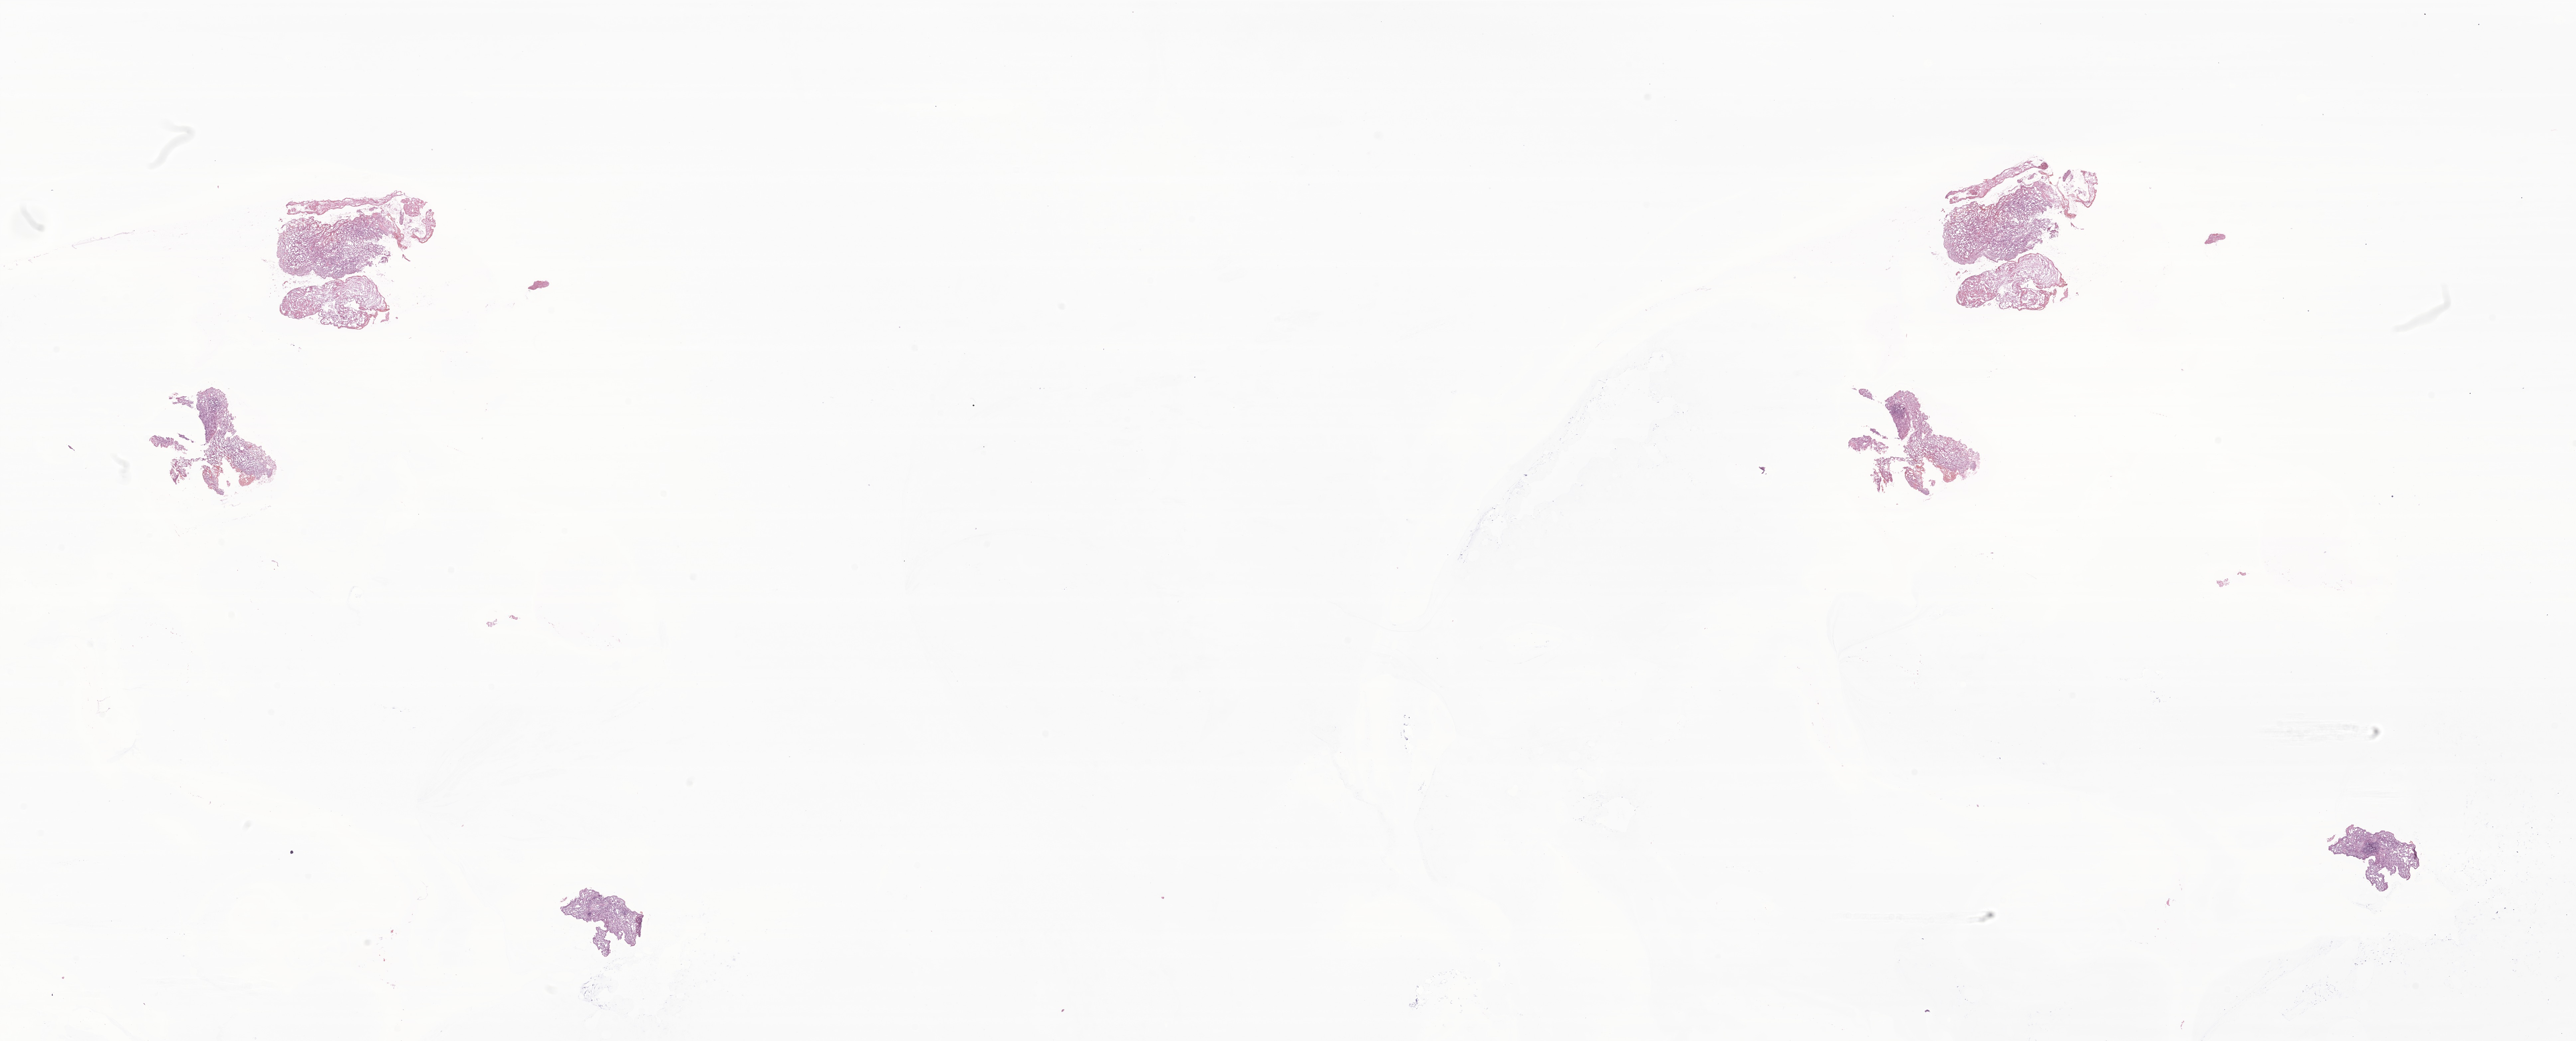
Digitized haematoxylin and eosin-stained section of tumor tissue from the soft tissue of upper extremity — a low-resolution overview of the entire scanned area, about 32.7 x 13.2 mm. Frozen section (OCT-embedded). Patient: female, age 184 months (15 years 4 months).
Recorded diagnosis: Synovial sarcoma, spindle cell. Tissue or organ of origin (case record): connective, subcutaneous and other soft tissues of upper limb and shoulder.